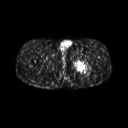
FDG PET of an extremity soft-tissue mass (from a PET/CT study), one axial slice. Slice 256 of 267 in the series (ordered by position). 128 × 128 image matrix, field of view 500 × 500 mm. Patient: male, 27 years. Case-level facts recorded for this patient, not image findings: histological type: extraskeletal osteosarcoma; grade: high; site of the primary tumour: left adductur.
Structures marked on this image (expert contour drawn on MRI and transferred to this co-registered scan by the dataset authors):
- gross tumour volume (mass): bounding box [x1, y1, x2, y2] px = [72, 52, 95, 74]